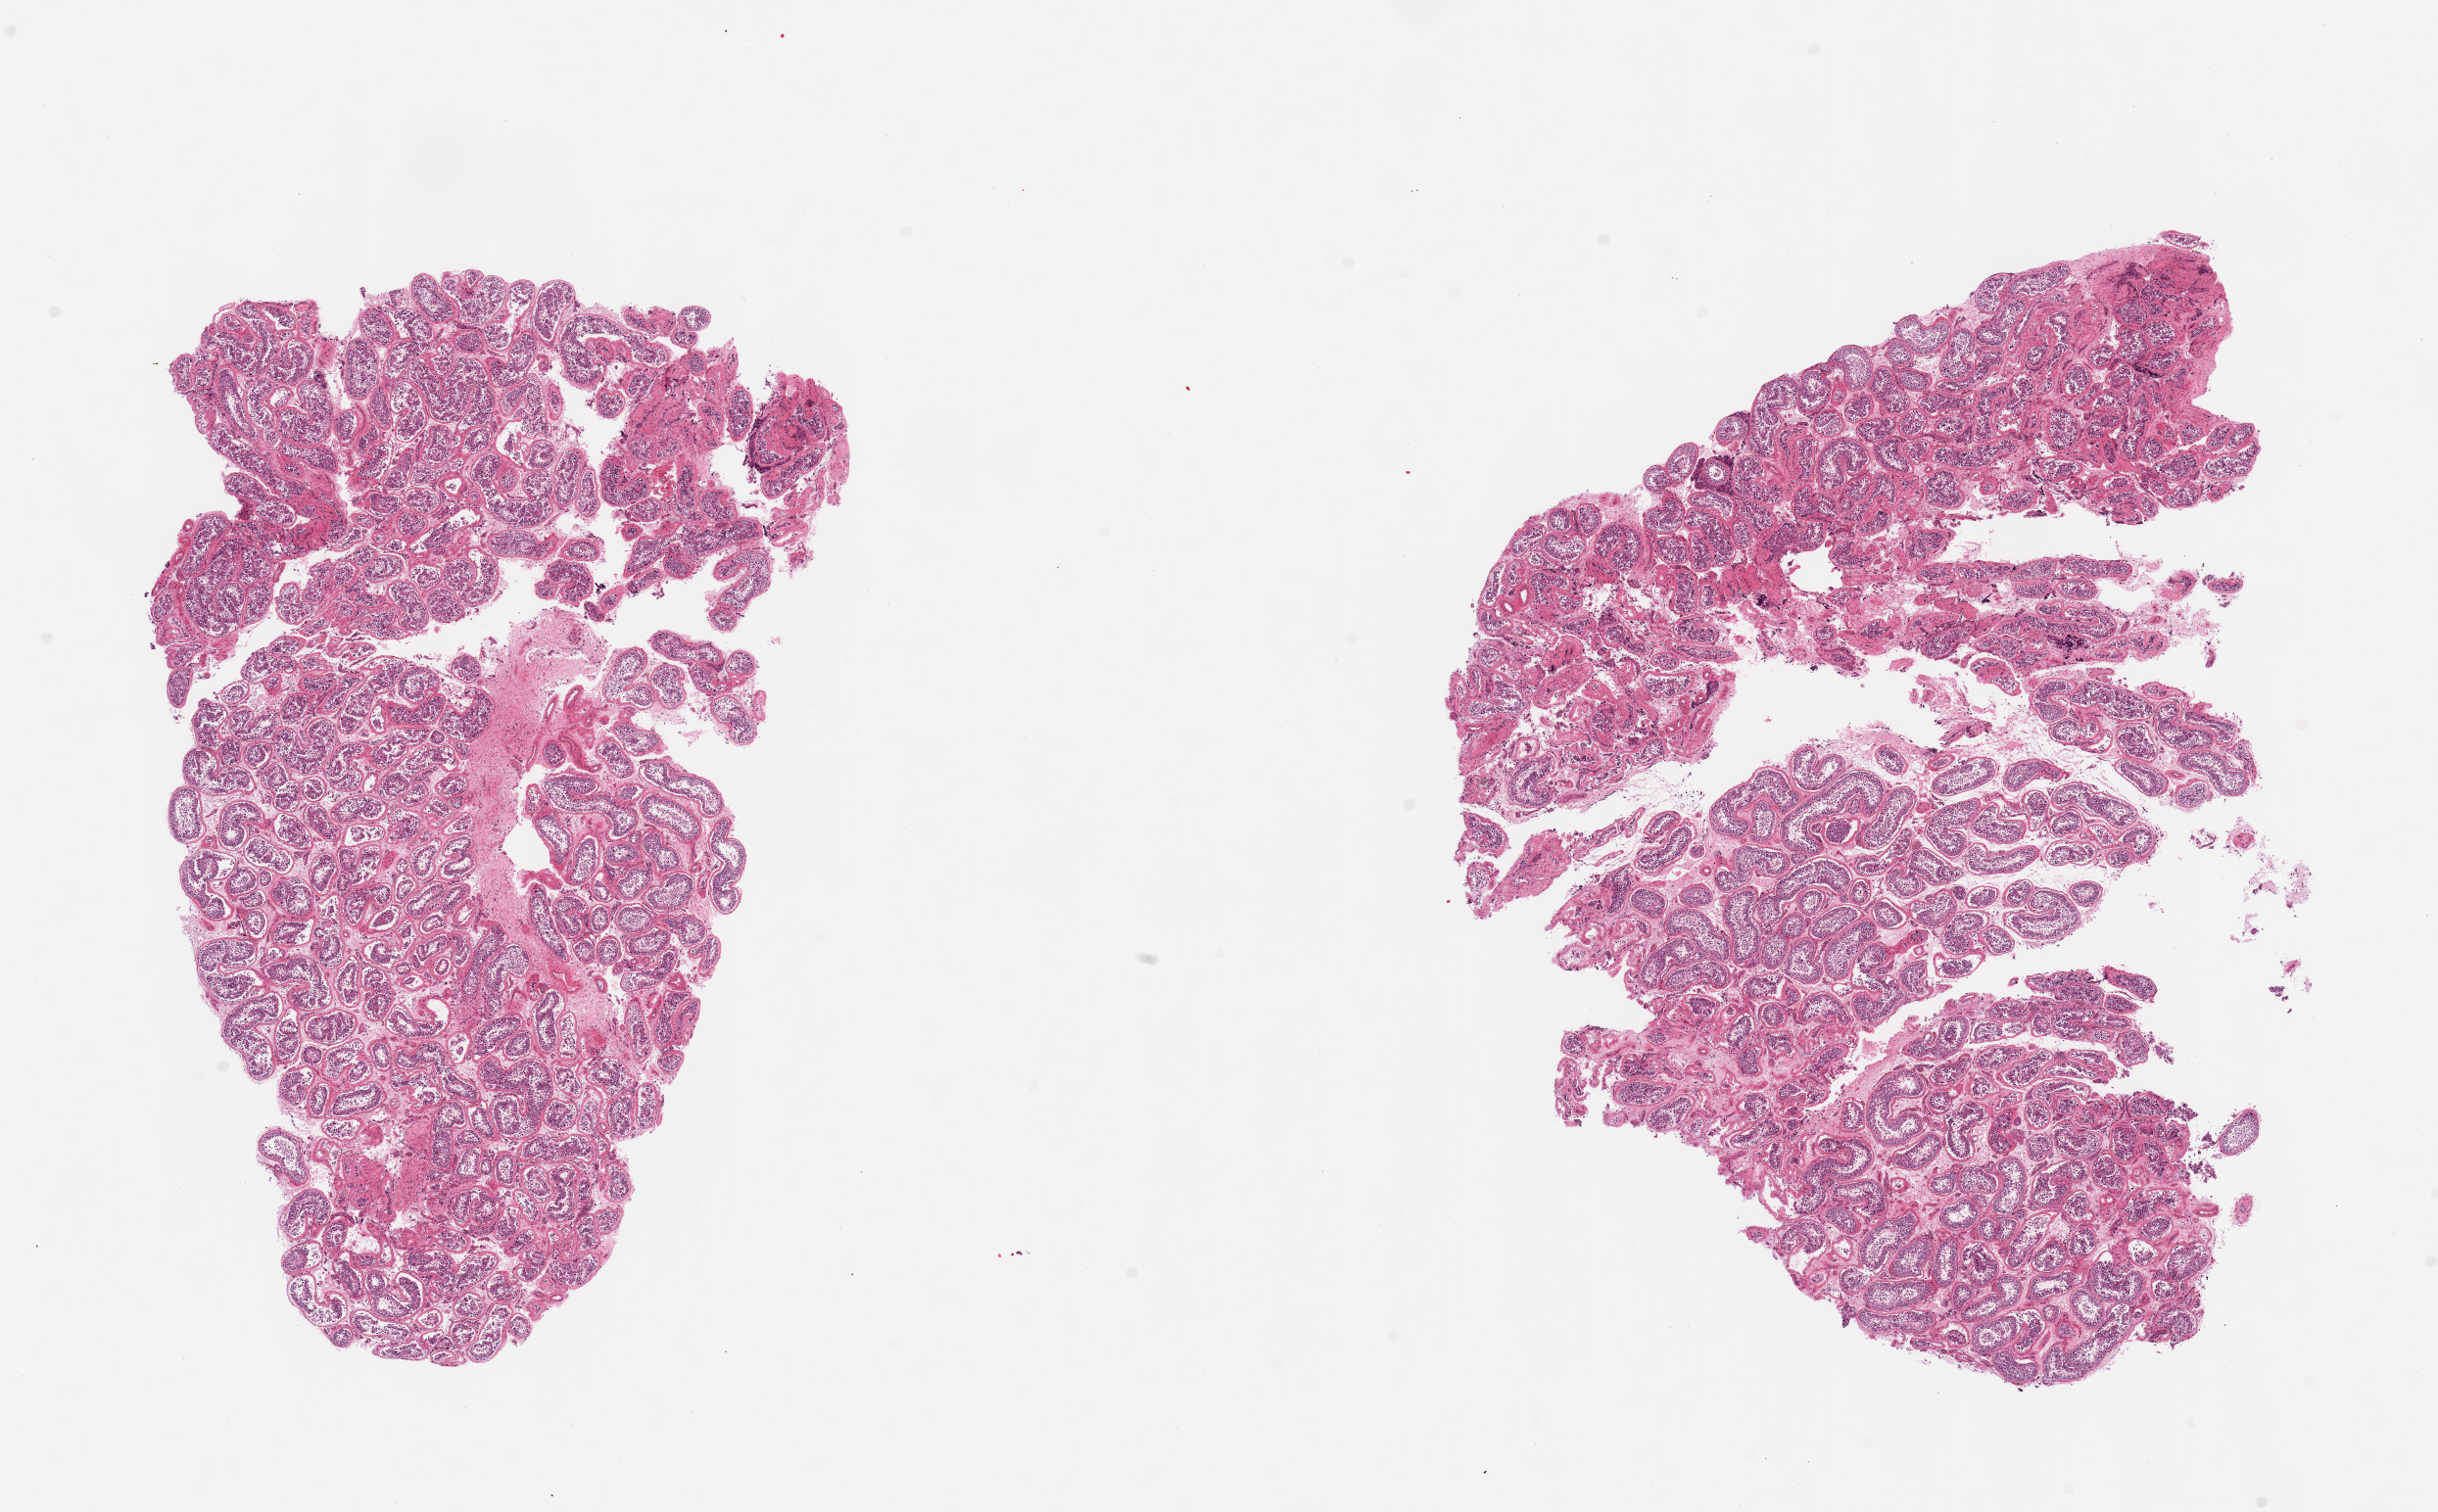
Whole-slide image, haematoxylin and eosin stain — whole scanned area (about 19.7 x 12.2 mm, from a 20x scan) shown as a low-resolution overview; PAXgene-fixed, paraffin-embedded tissue; target tissue: testis; tissue donor sample. Donor: male.
Review note (as recorded): 2 pieces, spermatogenesis is present but appears reduced.